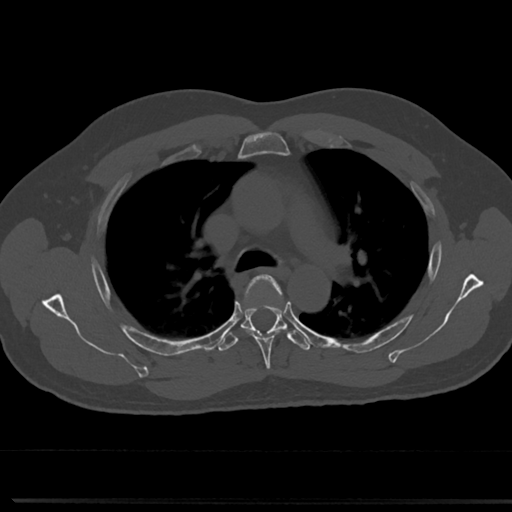
CT including the spine, one axial slice; position 522 of 817 along the scan axis; reconstruction kernel Br40s/3; bone window (W 1800 / L 400 HU); 0.5 mm slice thickness; 512 × 512 image matrix, field of view 355 × 355 mm. Patient: male, 61 years. Case-level facts recorded for this patient, not image findings: primary cancer: prostate.
Annotated regions visible in this slice (semi-automatically segmented with operator editing):
- T4 vertebra: bounding box <239,275,288,361> (left, top, right, bottom; pixels)
- T5 vertebra: <224,309,310,349>